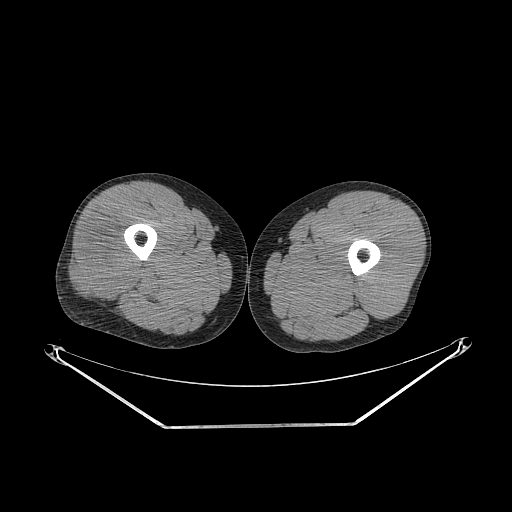
CT of an extremity soft-tissue mass (from a PET/CT study), one axial slice. Position 241 of 267 along the scan axis. Soft-tissue window (W 400 / L 40 HU). 3.75 mm slice thickness. 512 × 512 image matrix. Male patient. Case-level facts recorded for this patient, not image findings: histological type: poorly differentiated synovial sarcoma; grade: high; site of the primary tumour: right buttock.
Annotated regions visible in this slice (expert contour drawn on MRI and transferred to this co-registered scan by the dataset authors):
- gross tumour volume including surrounding oedema: bounding box [x1, y1, x2, y2] px = [73, 224, 136, 300]
- gross tumour volume (mass): [75, 224, 136, 300]